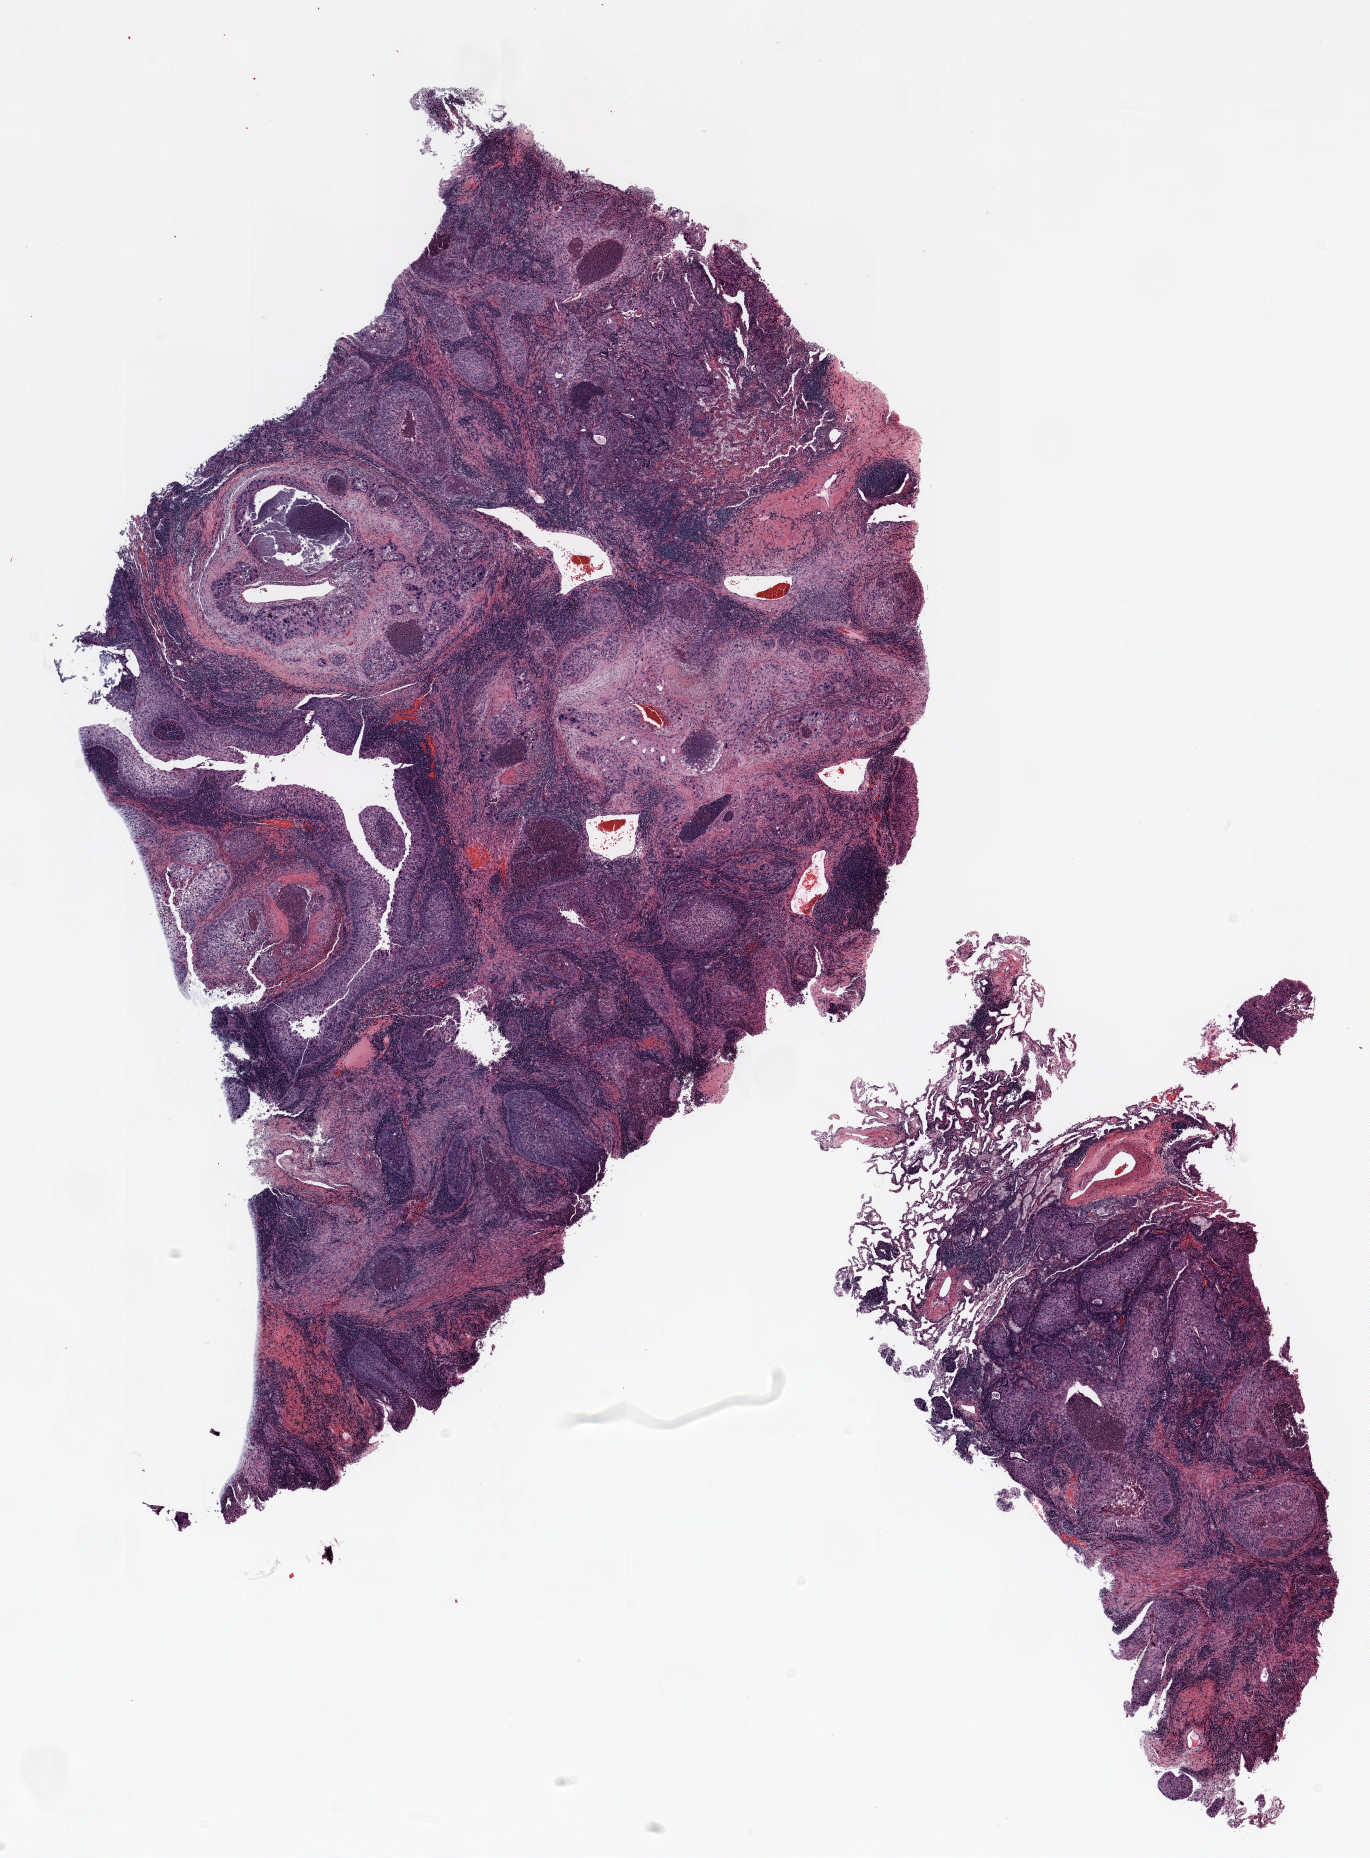
H&E whole-slide image, low-resolution overview of the scanned area, about 11.0 x 14.9 mm; formalin-fixed paraffin-embedded (FFPE) section; lung. Male, age 73 at enrolment. Current smoker at enrolment. Grade: poorly differentiated (G3).
- tumour size (pathology): 25 mm
- primary tumour location (clinical record): left lower lobe
- stage (AJCC 6th edition): IA
- participant's lung-cancer diagnosis: Squamous cell carcinoma, NOS